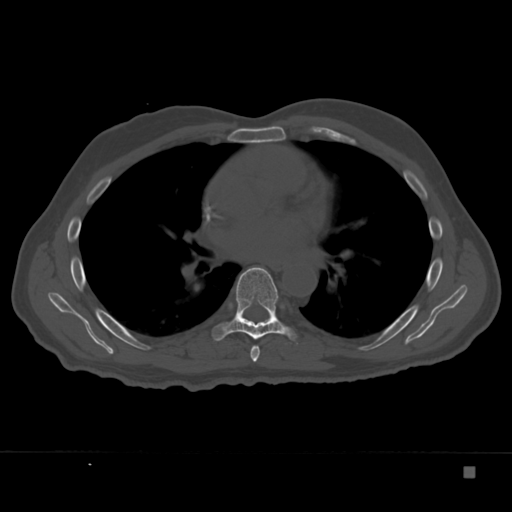
CT including the spine, one axial slice; slice 225 of 332 in the series (ordered by position); reconstruction kernel Br40s; 120 kVp; bone window (W 1800 / L 400 HU); 1.5 mm slice thickness; 512 × 512 image matrix, field of view 389 × 389 mm. Patient: male, 72 years. From the clinical record (not read from this slice): primary cancer: skeletal.
Outlined on this slice (semi-automatic segmentation, software-assisted and operator-edited):
- T6 vertebra: bounding box [x1, y1, x2, y2] px = [250, 345, 260, 362]
- T7 vertebra: [212, 267, 296, 341]